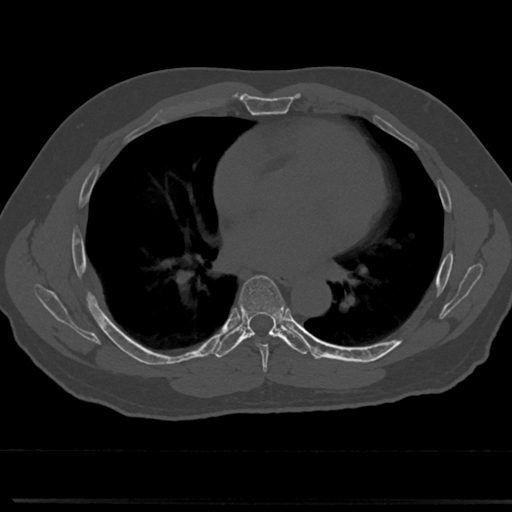
CT including the spine, one axial slice; slice 421 of 817 in the series (ordered by position); 120 kVp; bone window (W 1800 / L 400 HU); 0.5 mm slice thickness; 512 × 512 image matrix. Patient: male, 61 years. Case-level facts recorded for this patient, not image findings: primary cancer: prostate.
Annotated regions visible in this slice (semi-automatic segmentation, software-assisted and operator-edited):
- T6 vertebra: bounding box (x1, y1, x2, y2) in pixels: (240, 275, 287, 361)
- T7 vertebra: (239, 286, 286, 335)